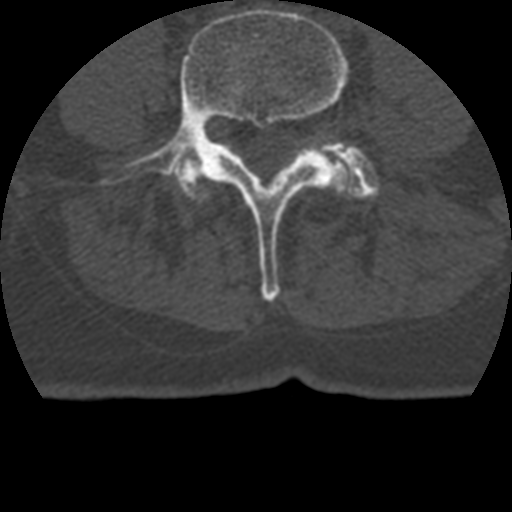
CT including the spine, one axial slice; position 63 of 399 along the scan axis; reconstruction kernel STANDARD; bone window (W 1800 / L 400 HU); 512 × 512 image matrix, field of view 160 × 160 mm. Patient age 69 years. From the clinical record (not read from this slice): primary cancer: prostate.
Structures marked on this image (semi-automatic segmentation, software-assisted and operator-edited):
- L4 vertebra: box from (x=105, y=8) to (x=348, y=301) px
- L5 vertebra: (x=332, y=143)–(x=379, y=198)